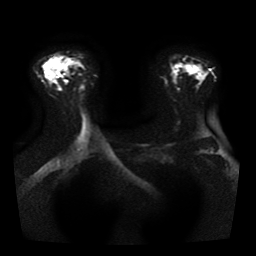
Breast MRI, one axial slice; position 27 of 41 along the scan axis; diffusion-weighted series; image 2 of 4 stored at this slice position (different b-values; order by instance number); 1.5 T; 256 × 256 image matrix, field of view 330 × 330 mm. Female patient.
Structures marked on this image (manually delineated by an expert):
- tumour on diffusion-weighted imaging: box from (x=64, y=80) to (x=68, y=83) px